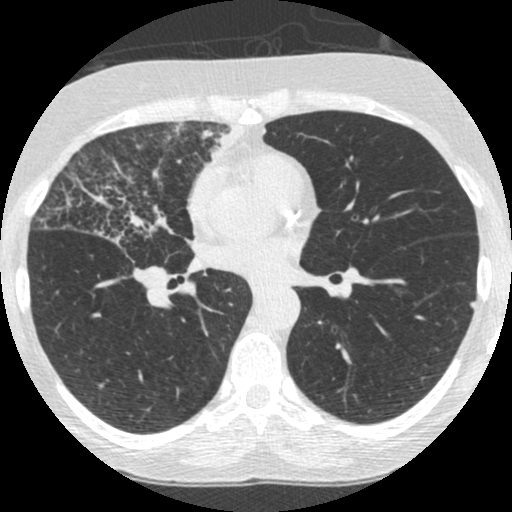
Low-dose screening chest CT, one axial slice; slice 131 of 253 in the series (ordered by position); 120 kVp; lung window (W 1500 / L -600 HU); 1.25 mm slice thickness; 512 × 512 image matrix, field of view 294 × 294 mm.
Outlined on this slice (manually delineated by an expert):
- lesion 4 (tumor, upper lobe of right lung): bounding box [x1, y1, x2, y2] px = [200, 123, 245, 160]